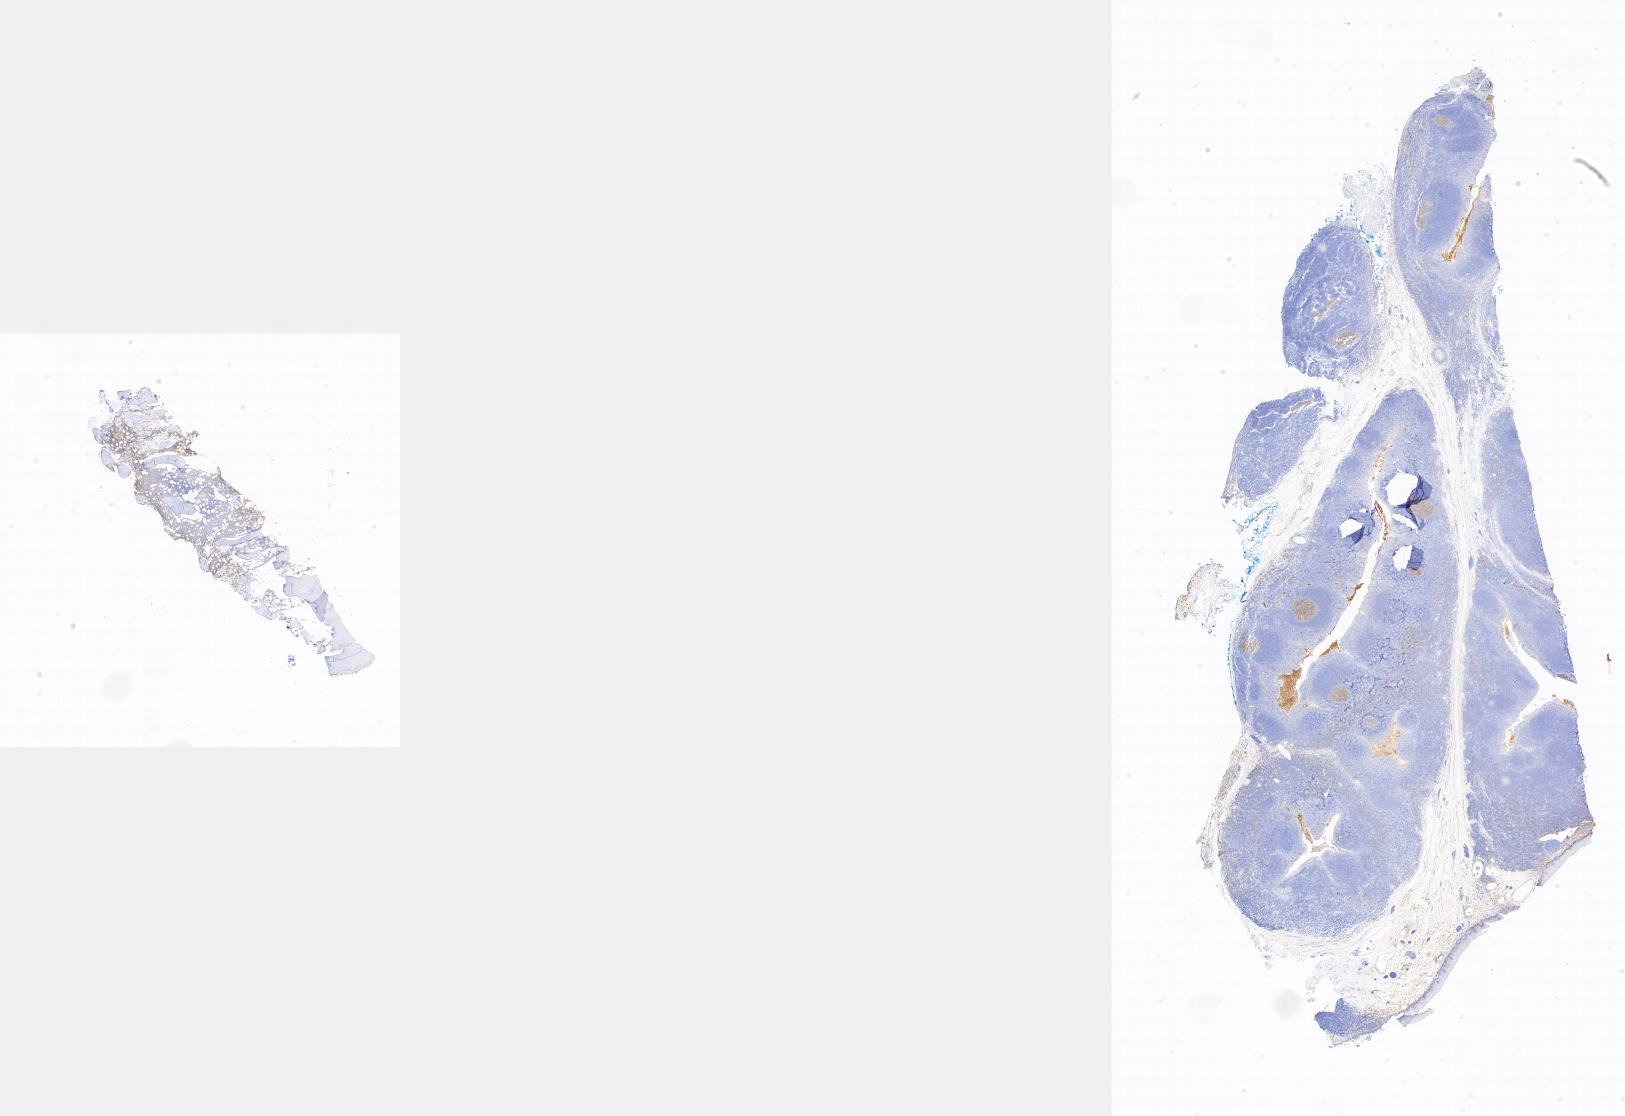
Whole-slide image, immunohistochemical stain for CD10, whole scanned area shown as a low-resolution overview. Specimen: tumor tissue. Anatomic site: bone marrow. Female, age 4 years at initial diagnosis.
- diagnosis: Burkitt lymphoma, NOS